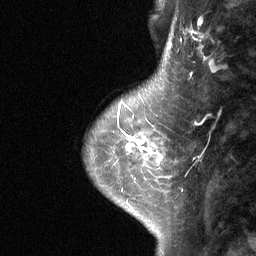
Breast MRI (dynamic contrast-enhanced), one sagittal slice. Position 16 of 64 along the scan axis. Dynamic contrast-enhanced study with each time point stored as its own series, time point 2 of 3 at this slice position (early post-contrast, ordered by acquisition time). 1.5 T. TE 4.8 ms, TR 27 ms. 256 × 256 image matrix, field of view 180 × 180 mm. Female patient, age 42 years. From the clinical record (not read from this slice): setting: breast cancer imaged before/during neoadjuvant chemotherapy; receptor status: triple-negative.
Outlined on this slice (semi-automatic segmentation, software-assisted and operator-edited):
- analysis volume of interest (the breast-tissue region the enhancement analysis was run in; not a lesion): bounding box (x1, y1, x2, y2) in pixels: (111, 104, 172, 178)
- tumour enhancement mask (voxels above the 90 % enhancement threshold inside the analysis volume of interest): (123, 132, 163, 164)